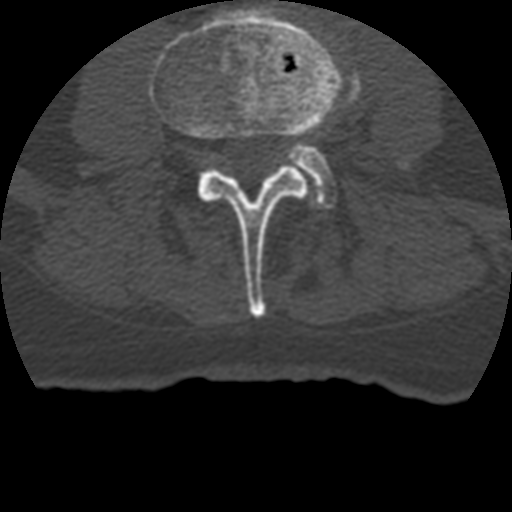
CT including the spine, one axial slice. Position 82 of 399 along the scan axis. Reconstruction kernel STANDARD. 120 kVp. Bone window (W 1800 / L 400 HU). 1.25 mm slice thickness. 512 × 512 image matrix. Patient age 69 years. Case-level facts recorded for this patient, not image findings: primary cancer: prostate.
Structures marked on this image (semi-automatically segmented with operator editing):
- L3 vertebra: bounding box <149,6,343,318> (left, top, right, bottom; pixels)
- L4 vertebra: <288,76,408,213>